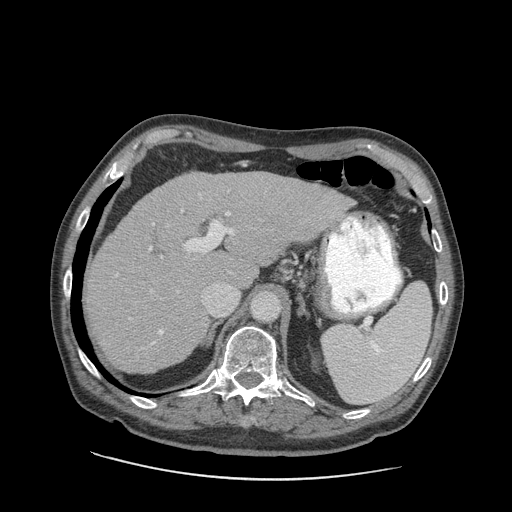
Contrast-enhanced abdominal CT (liver protocol), one axial slice; position 61 of 89 along the scan axis; reconstruction kernel STANDARD; soft-tissue window (W 400 / L 40 HU); 512 × 512 image matrix, field of view 420 × 420 mm. Case-level facts recorded for this patient, not image findings: diagnosis: hepatocellular carcinoma (patient treated with transarterial chemoembolisation; whether this scan precedes or follows treatment is not stated here); TNM stage (as recorded): Stage-I; Child-Pugh class: A; tumour differentiation: moderately differentiated; tumour nodularity: uninodular.
Outlined on this slice (semi-automatically segmented with operator editing):
- liver parenchyma outside the tumour (the mass and vessels are separate outlines, so this box may not span the whole liver): bounding box (x1, y1, x2, y2) in pixels: (88, 172, 350, 374)
- liver vessels: (115, 189, 338, 350)